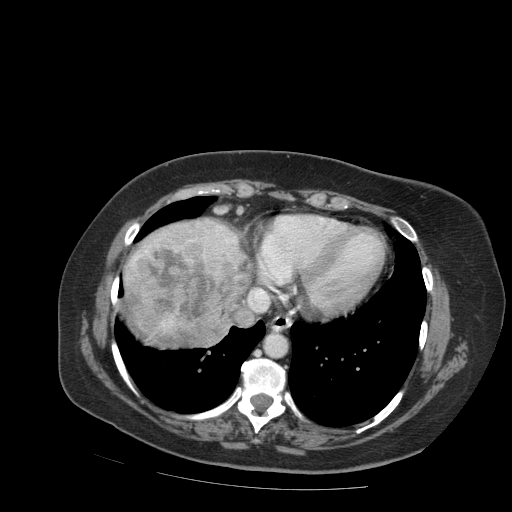
Contrast-enhanced abdominal CT (liver protocol), one axial slice. Slice 82 of 99 in the series (ordered by position). Reconstruction kernel STANDARD. Soft-tissue window (W 400 / L 40 HU). 512 × 512 image matrix, field of view 400 × 400 mm. Case-level facts recorded for this patient, not image findings: diagnosis: hepatocellular carcinoma (patient treated with transarterial chemoembolisation; whether this scan precedes or follows treatment is not stated here); TNM stage (as recorded): Stage-IVB; Child-Pugh class: A.
Structures marked on this image (semi-automatic segmentation, software-assisted and operator-edited):
- liver parenchyma outside the tumour (the mass and vessels are separate outlines, so this box may not span the whole liver): box from (x=122, y=218) to (x=246, y=346) px
- mass: (x=123, y=243)–(x=245, y=349)
- liver vessels: (x=189, y=226)–(x=236, y=255)